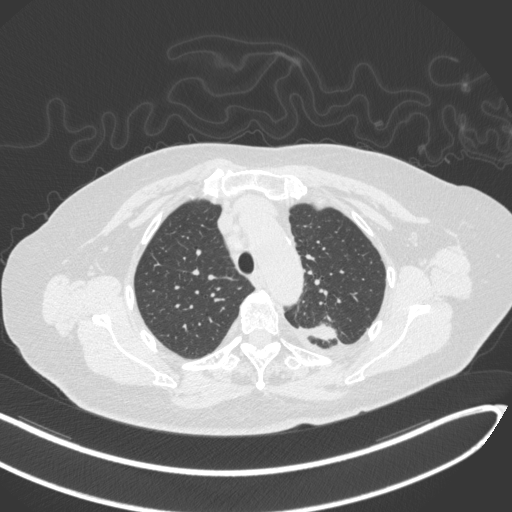
Chest CT, one axial slice; slice 245 of 270 in the series (ordered by position); reconstruction kernel B31f; lung window (W 1500 / L -600 HU); 1 mm slice thickness; 512 × 512 image matrix. Patient: female, 76 years. From the clinical record (not read from this slice): clinical TNM (as recorded): T1c N0 M0.
Annotated regions visible in this slice (bounding box drawn by a radiologist):
- lung tumour (recorded histology: adenocarcinoma): box from (x=305, y=314) to (x=342, y=344) px